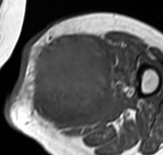
MRI of an extremity soft-tissue mass, one axial slice; position 37 of 65 along the scan axis; MR volume resampled by the dataset authors to the PET/CT grid (not the native acquisition matrix); 3.27 mm slice thickness; 163 × 155 image matrix, field of view 159 × 151 mm. Female patient. From the clinical record (not read from this slice): histological type: pleomorphic leiomyosarcoma; grade: high; site of the primary tumour: left thigh.
Outlined on this slice (expert contour drawn on MRI and transferred to this co-registered scan by the dataset authors):
- gross tumour volume including surrounding oedema: bounding box [x1, y1, x2, y2] px = [28, 35, 116, 132]
- gross tumour volume (mass): [28, 35, 111, 130]